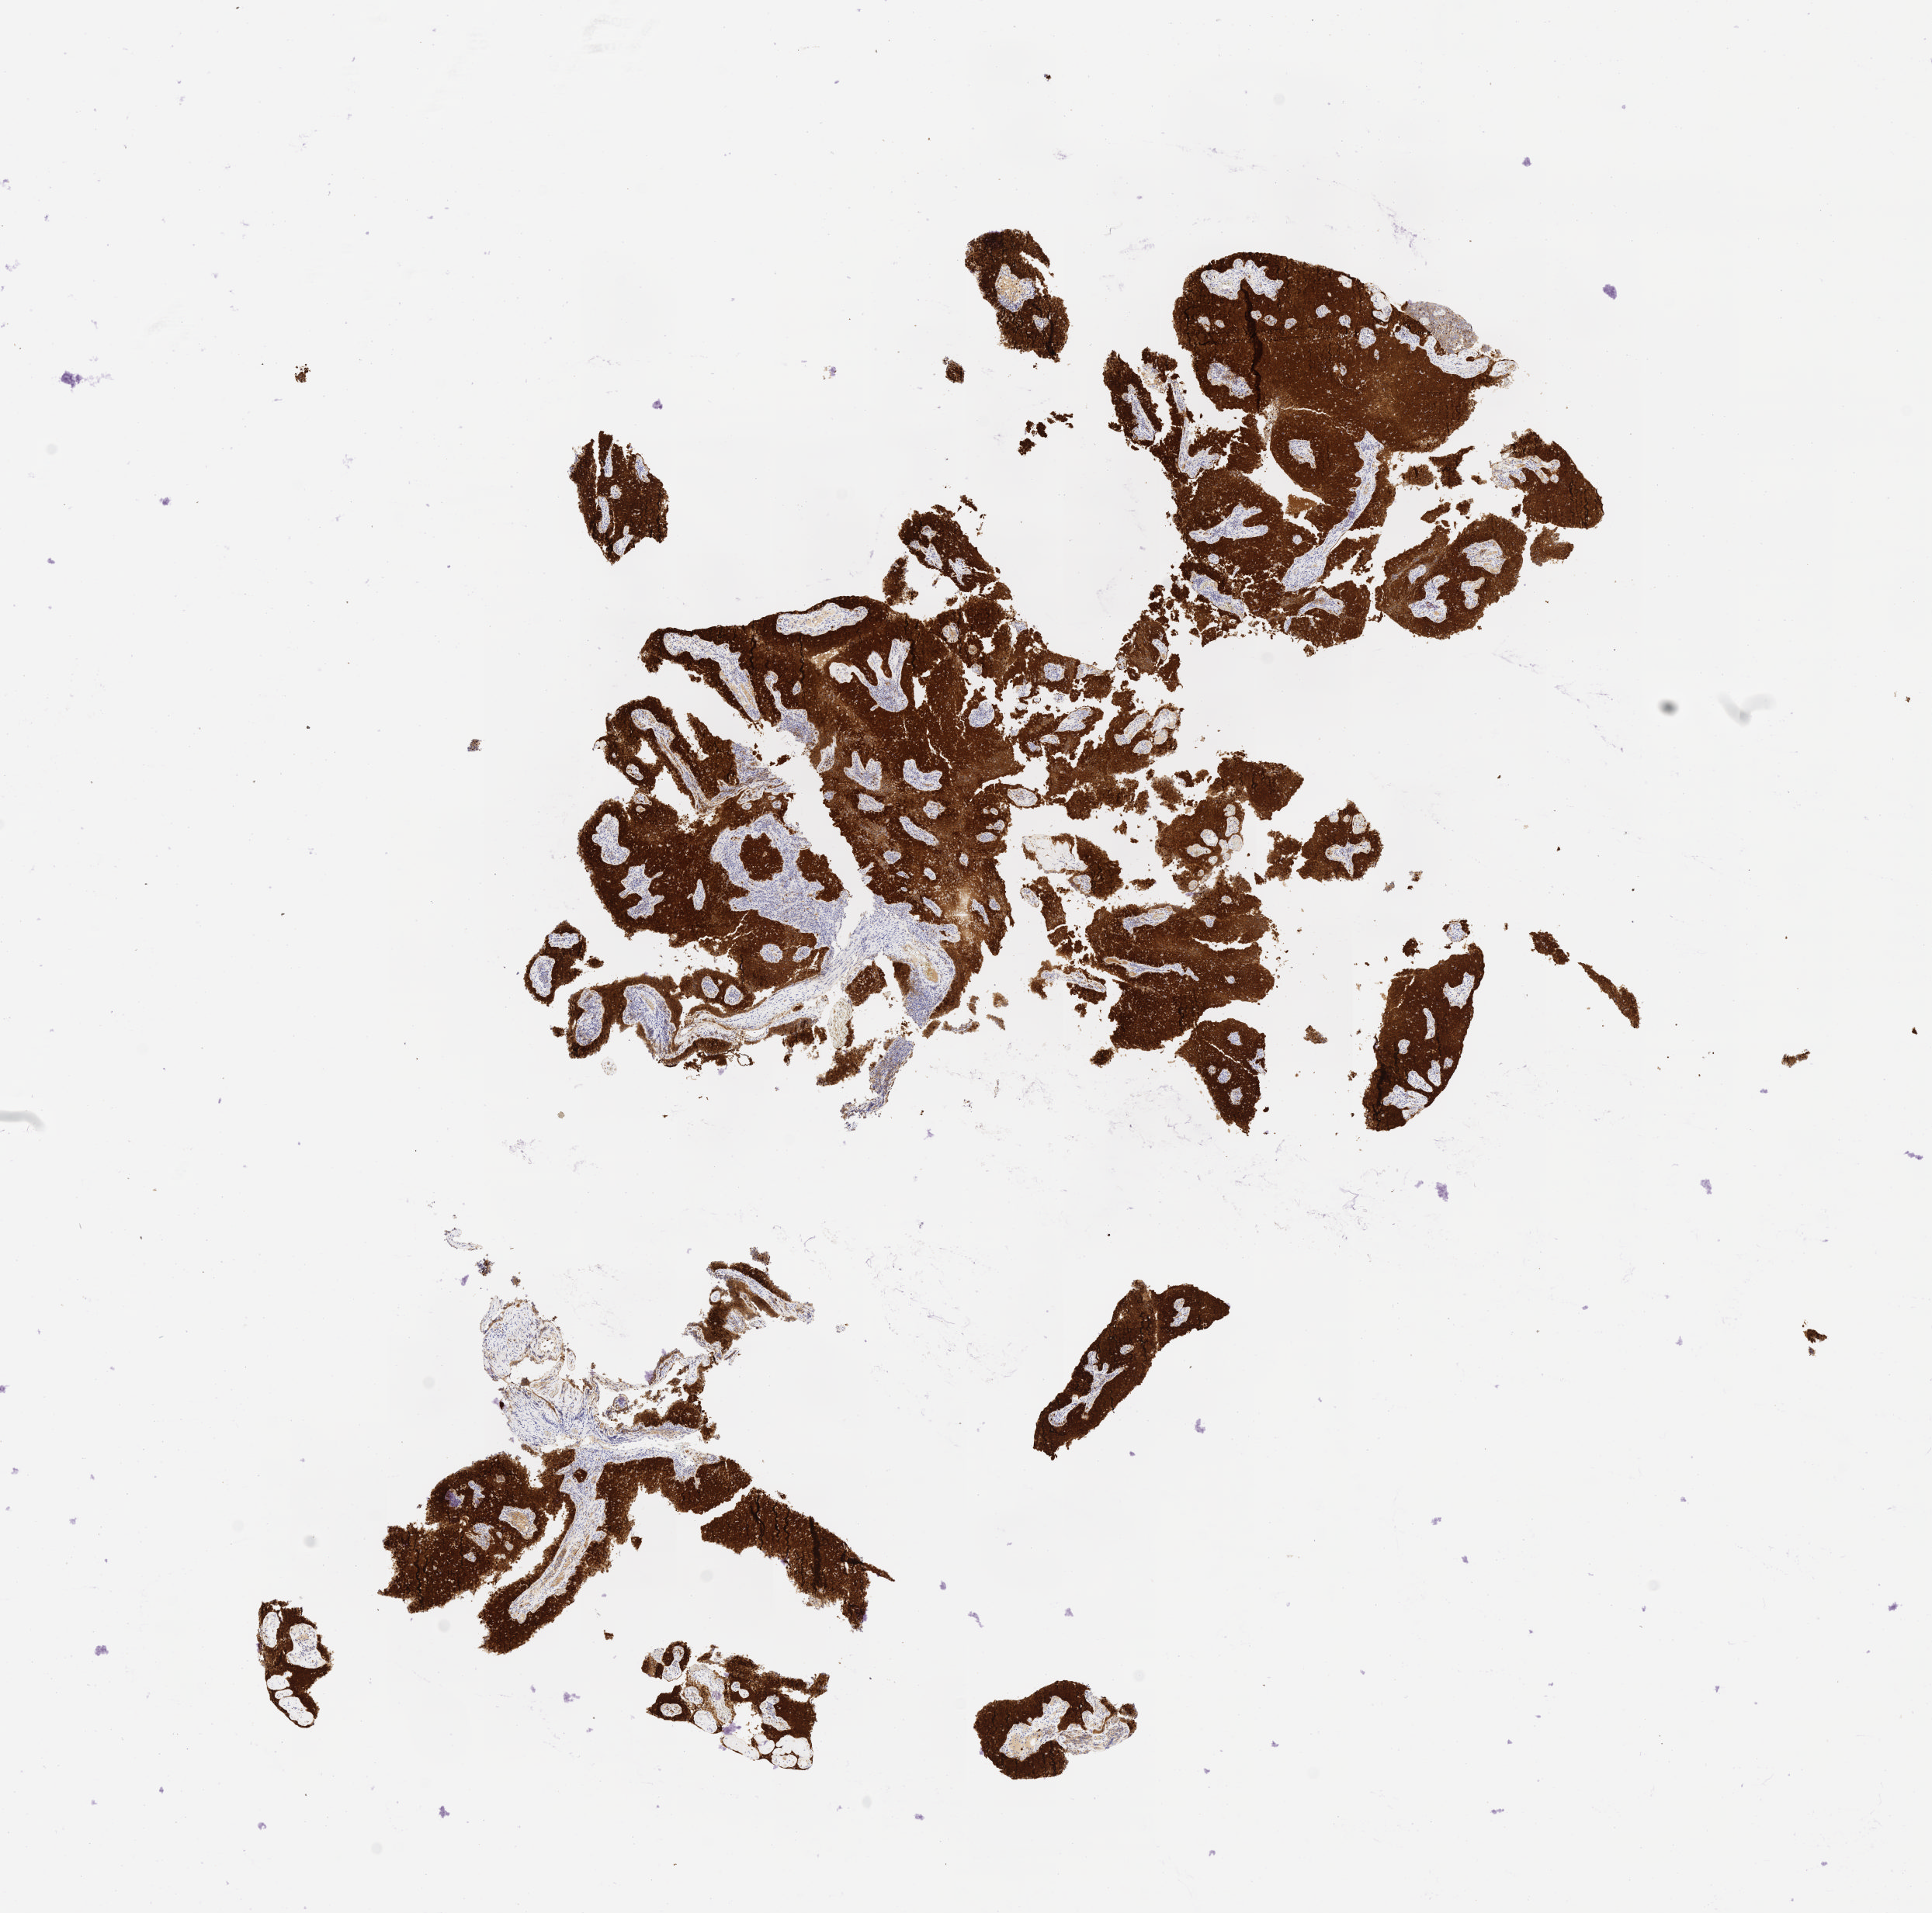
Immunohistochemistry (IHC) whole-slide image stained for p16 (p16INK4a), a low-resolution overview of the entire scanned area, about 10.1 x 10.0 mm. Specimen: tumor tissue. Site: cervix. Patient female; aged 80.
Diagnosis: Squamous cell carcinoma, large cell, nonkeratinizing, NOS.